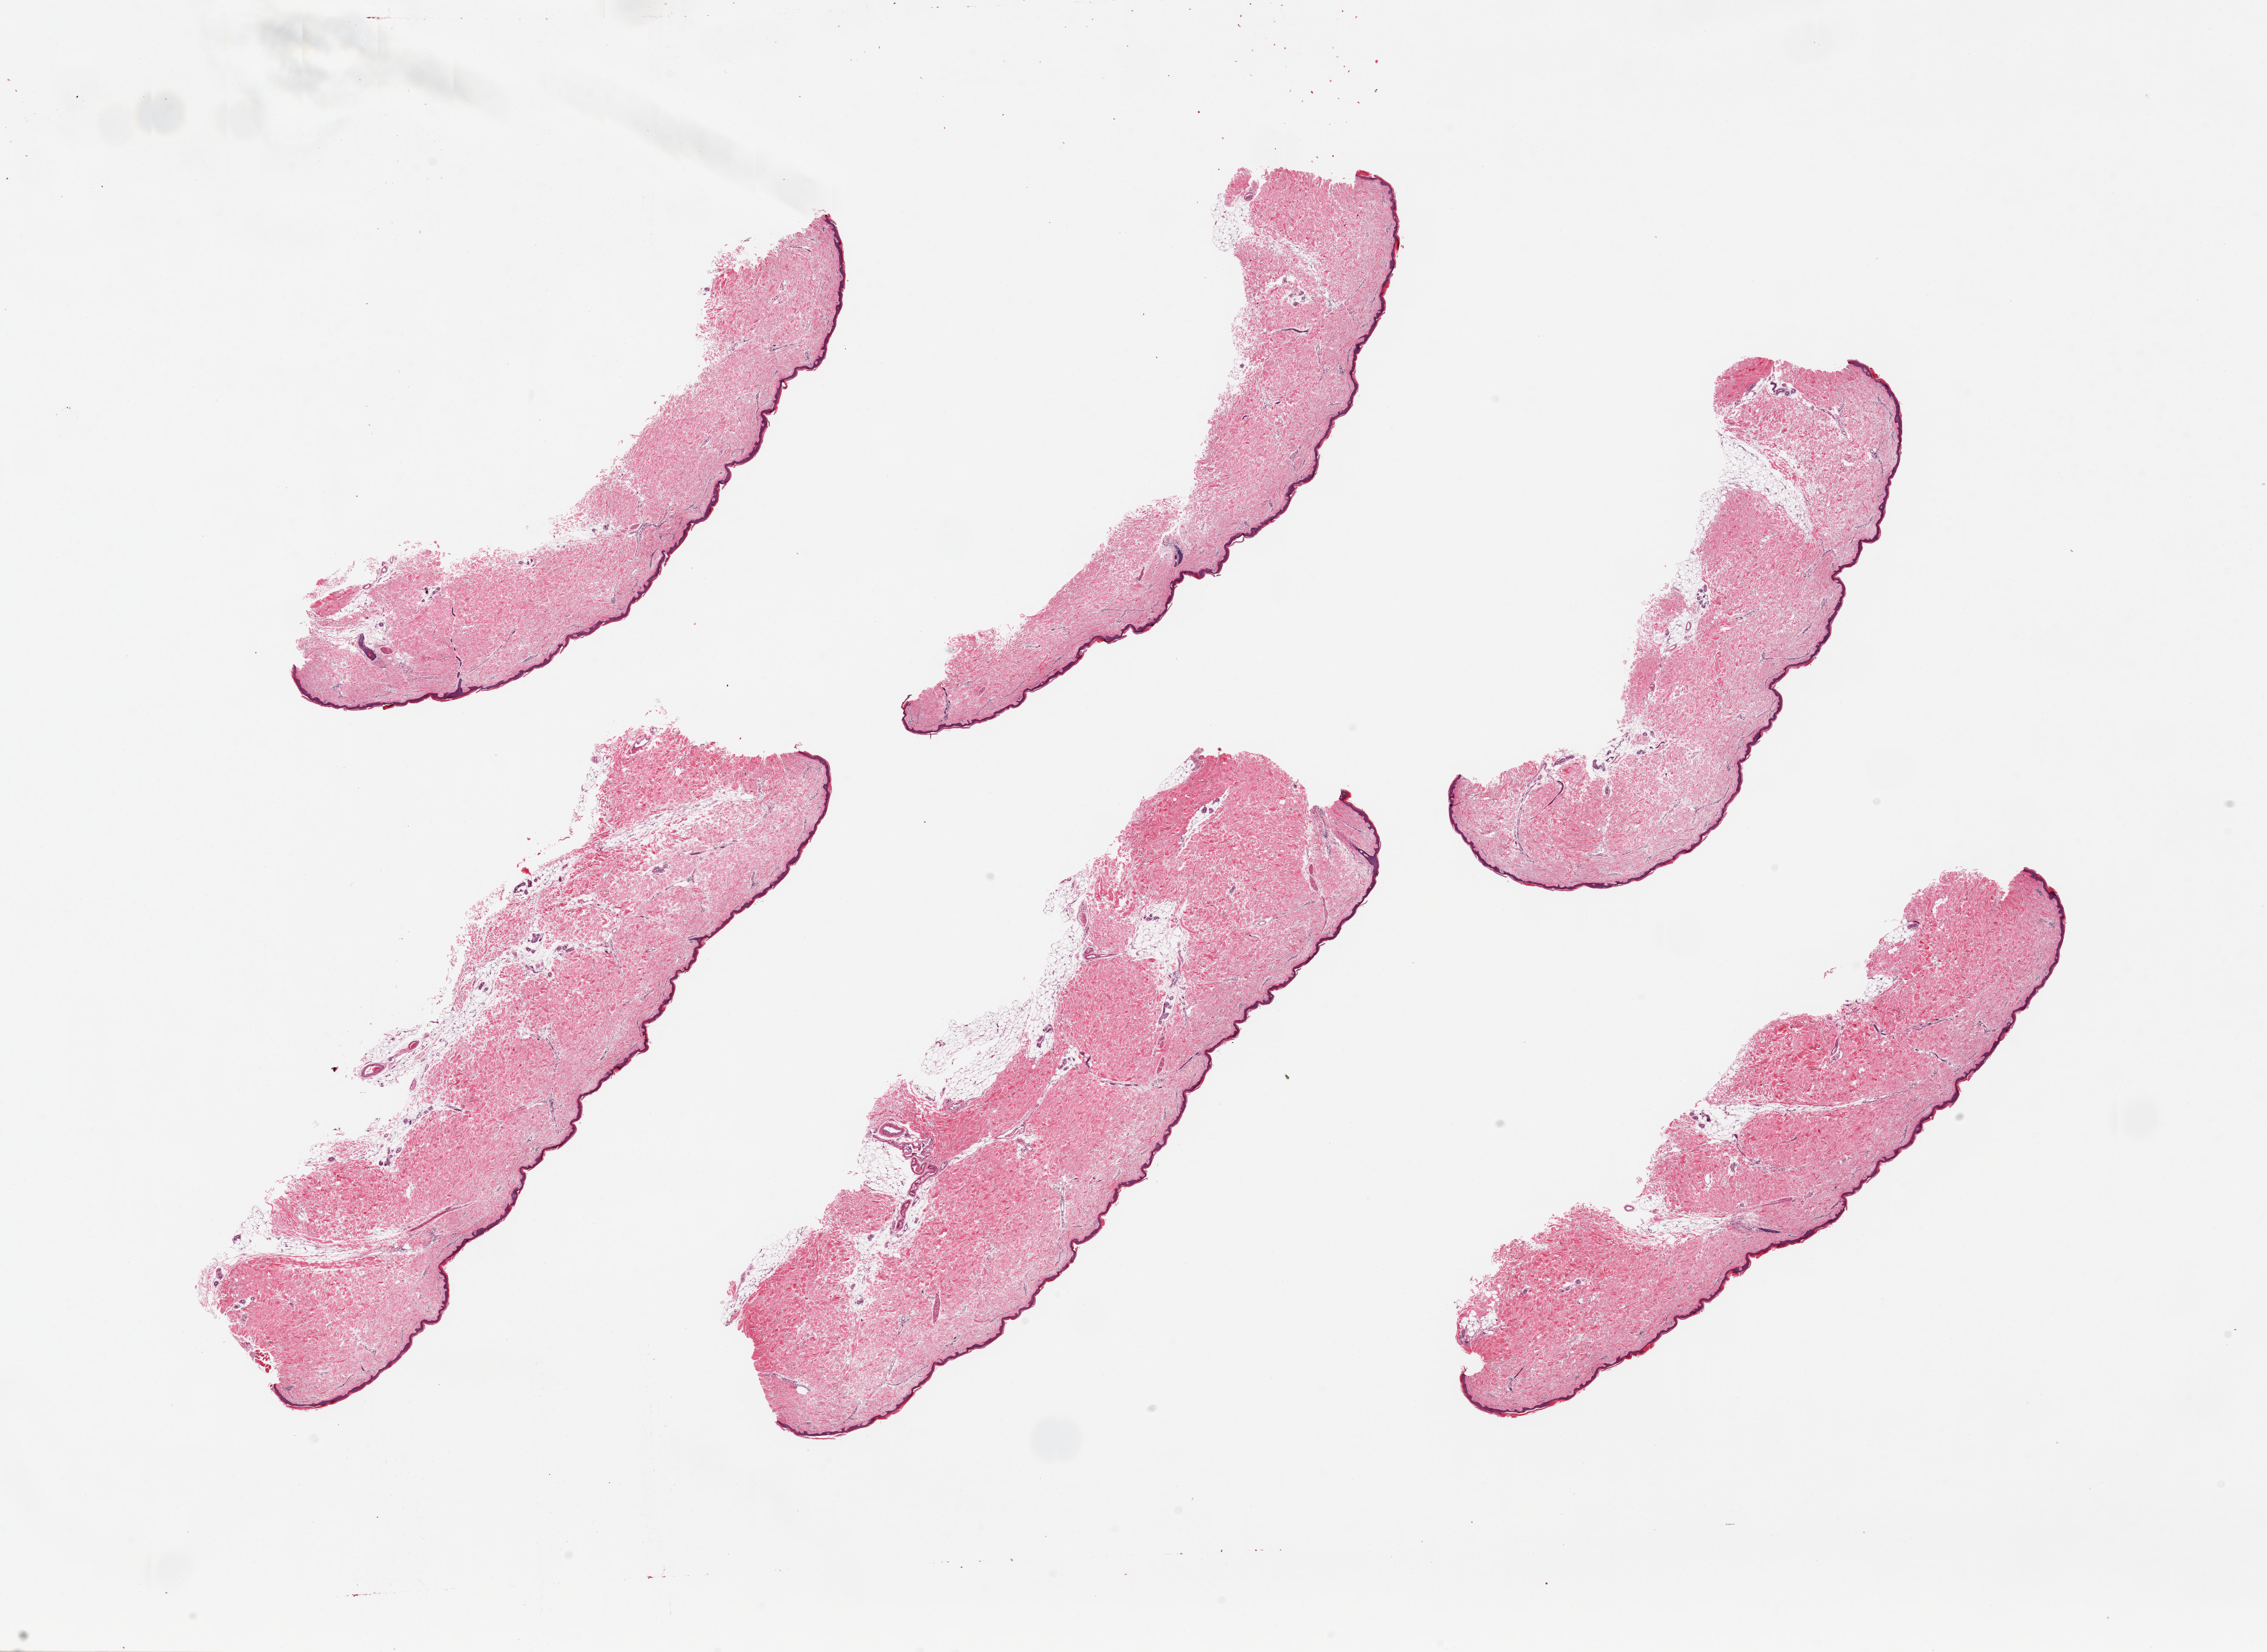
Digitized H&E-stained section — shown as a low-resolution overview of the whole scanned area (about 29.5 x 21.5 mm). PAXgene-fixed, paraffin-embedded tissue. Section of skin of lower leg (target tissue). Tissue donor sample. Donor: female.
Pathologist's review note for this sample: 6 pieces, up to 11x3.5mm; ~2% thickness is squamous epithelium.